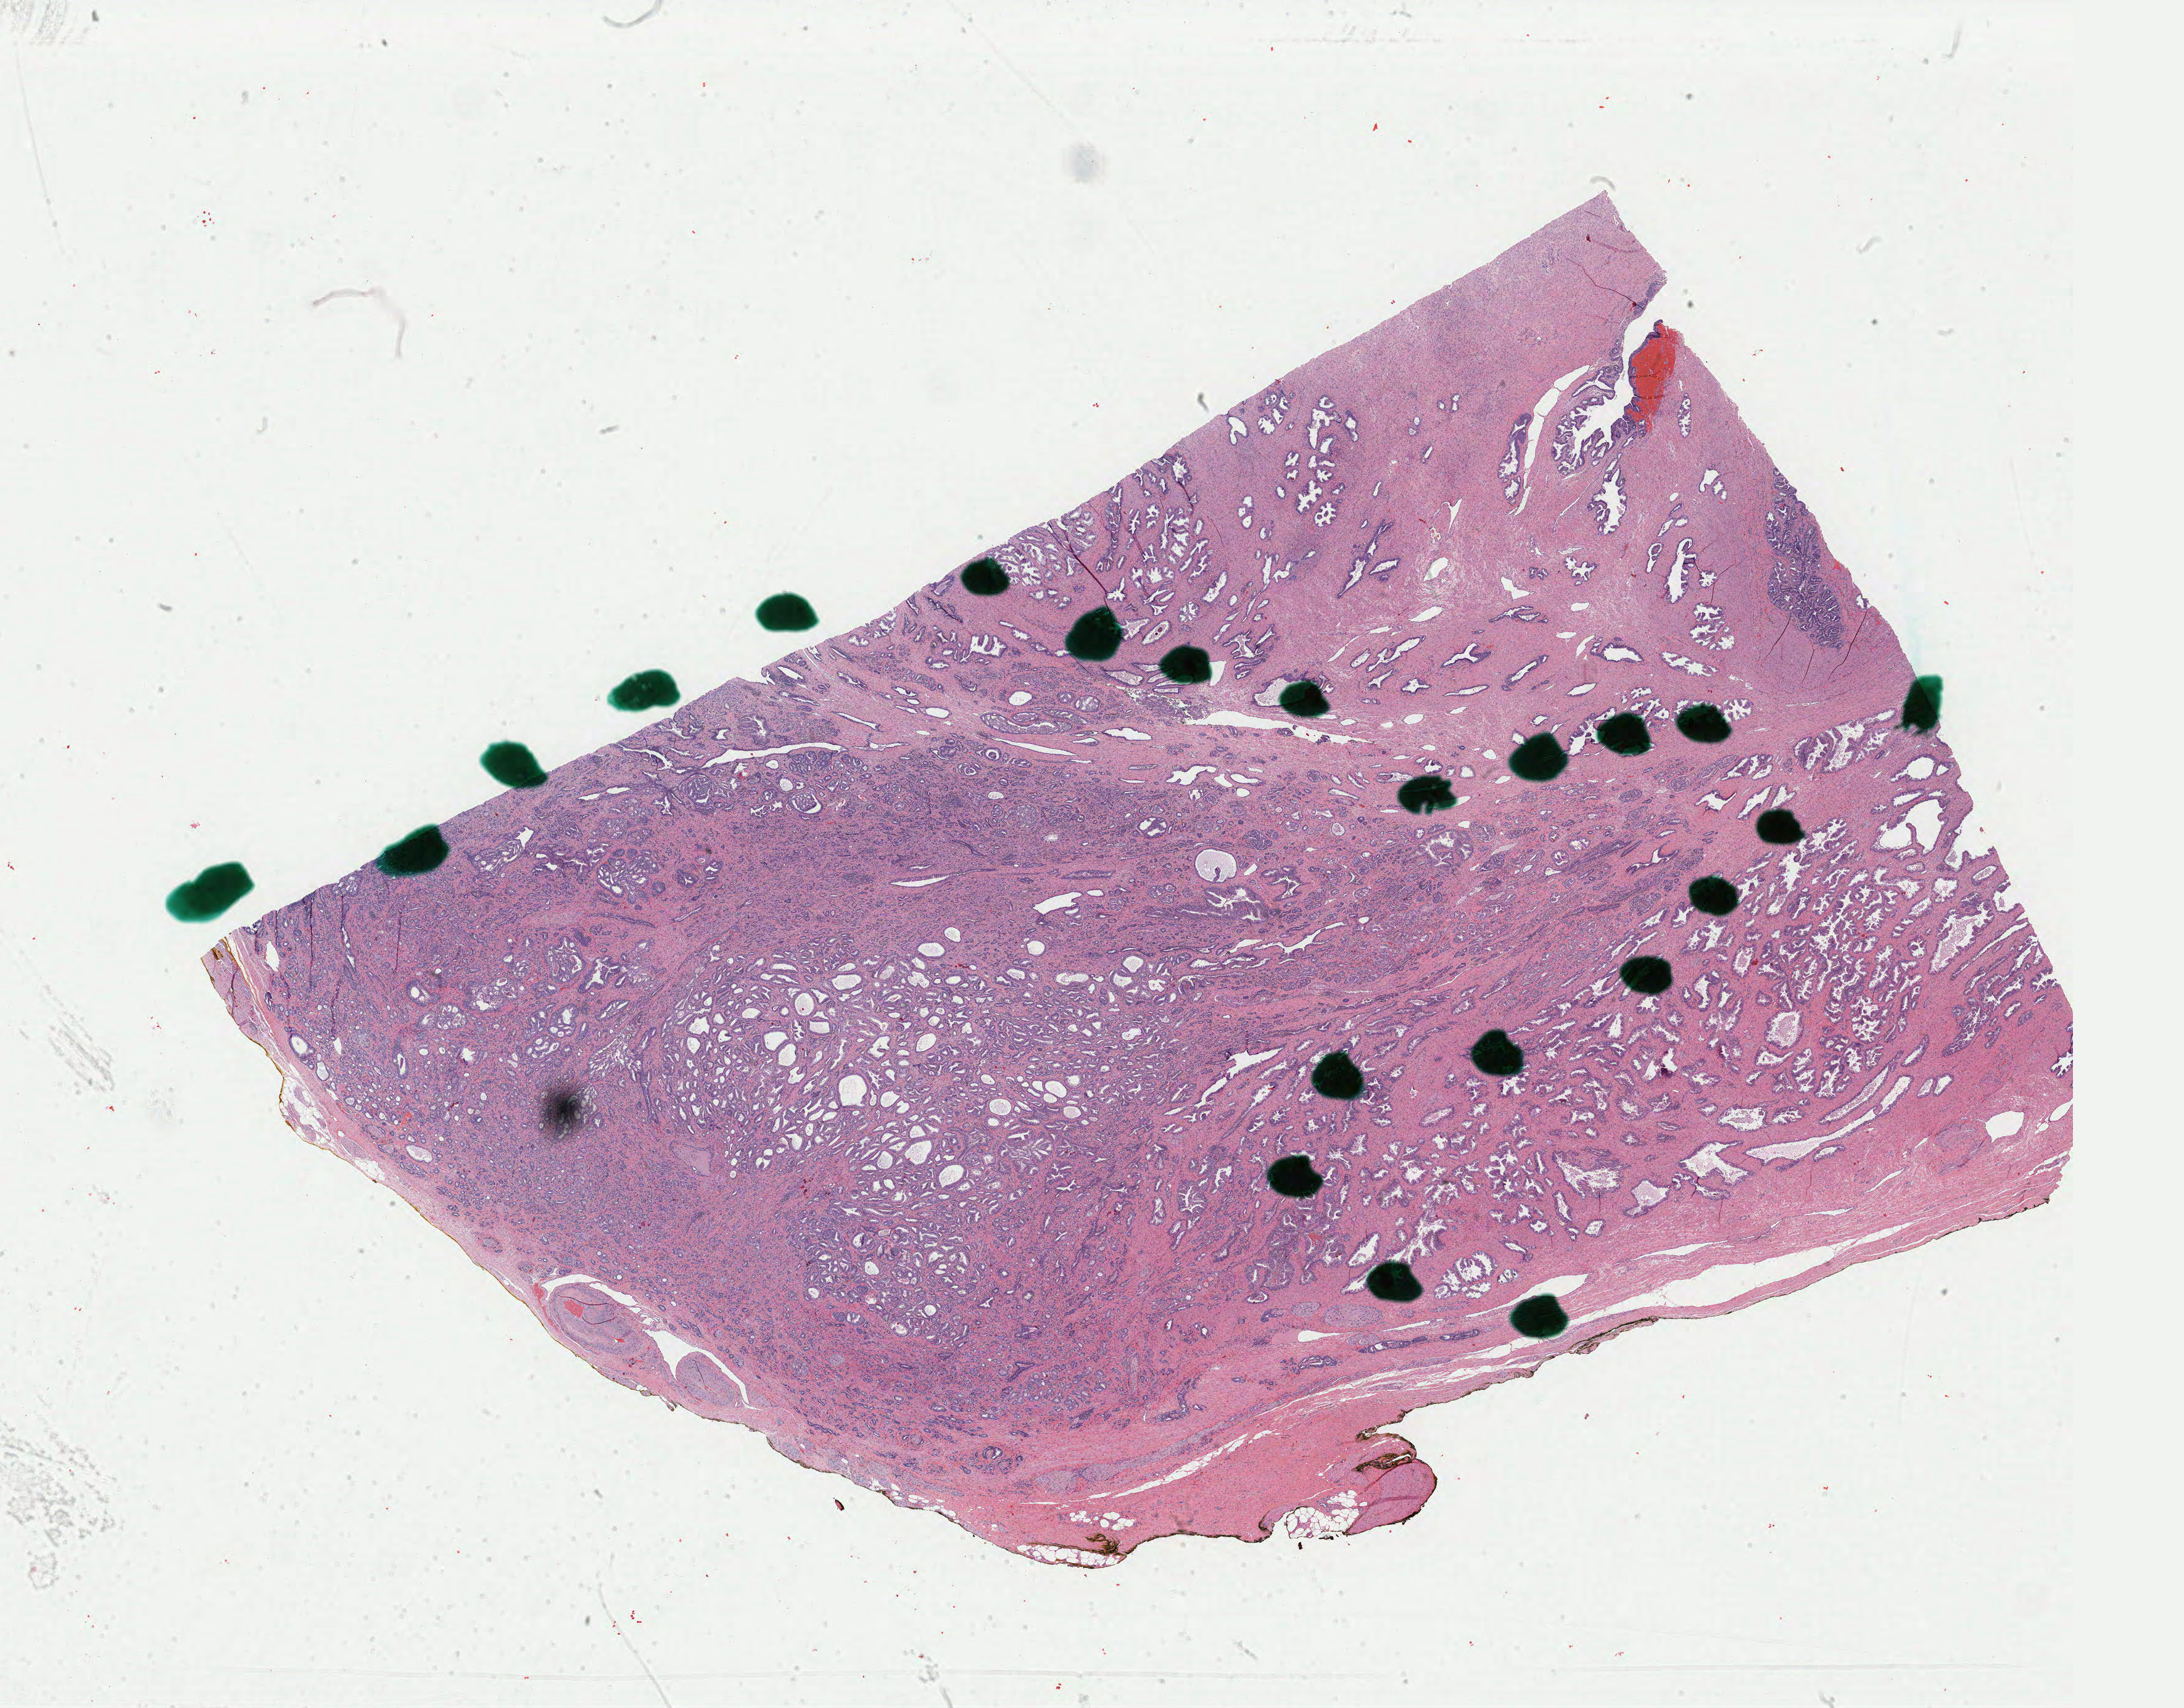
Hematoxylin and eosin (H&E) stained whole-slide image — low-resolution overview of the scanned area, about 28.1 x 22.0 mm; formalin-fixed paraffin-embedded (FFPE) diagnostic section; prostate, primary tumour sample. Male, age 58 years at initial diagnosis. Gleason score: 7 (4+3).
* lymph nodes positive (case pathology): 0 of 23 examined
* histologic diagnosis: Adenocarcinoma, NOS (prostate gland)